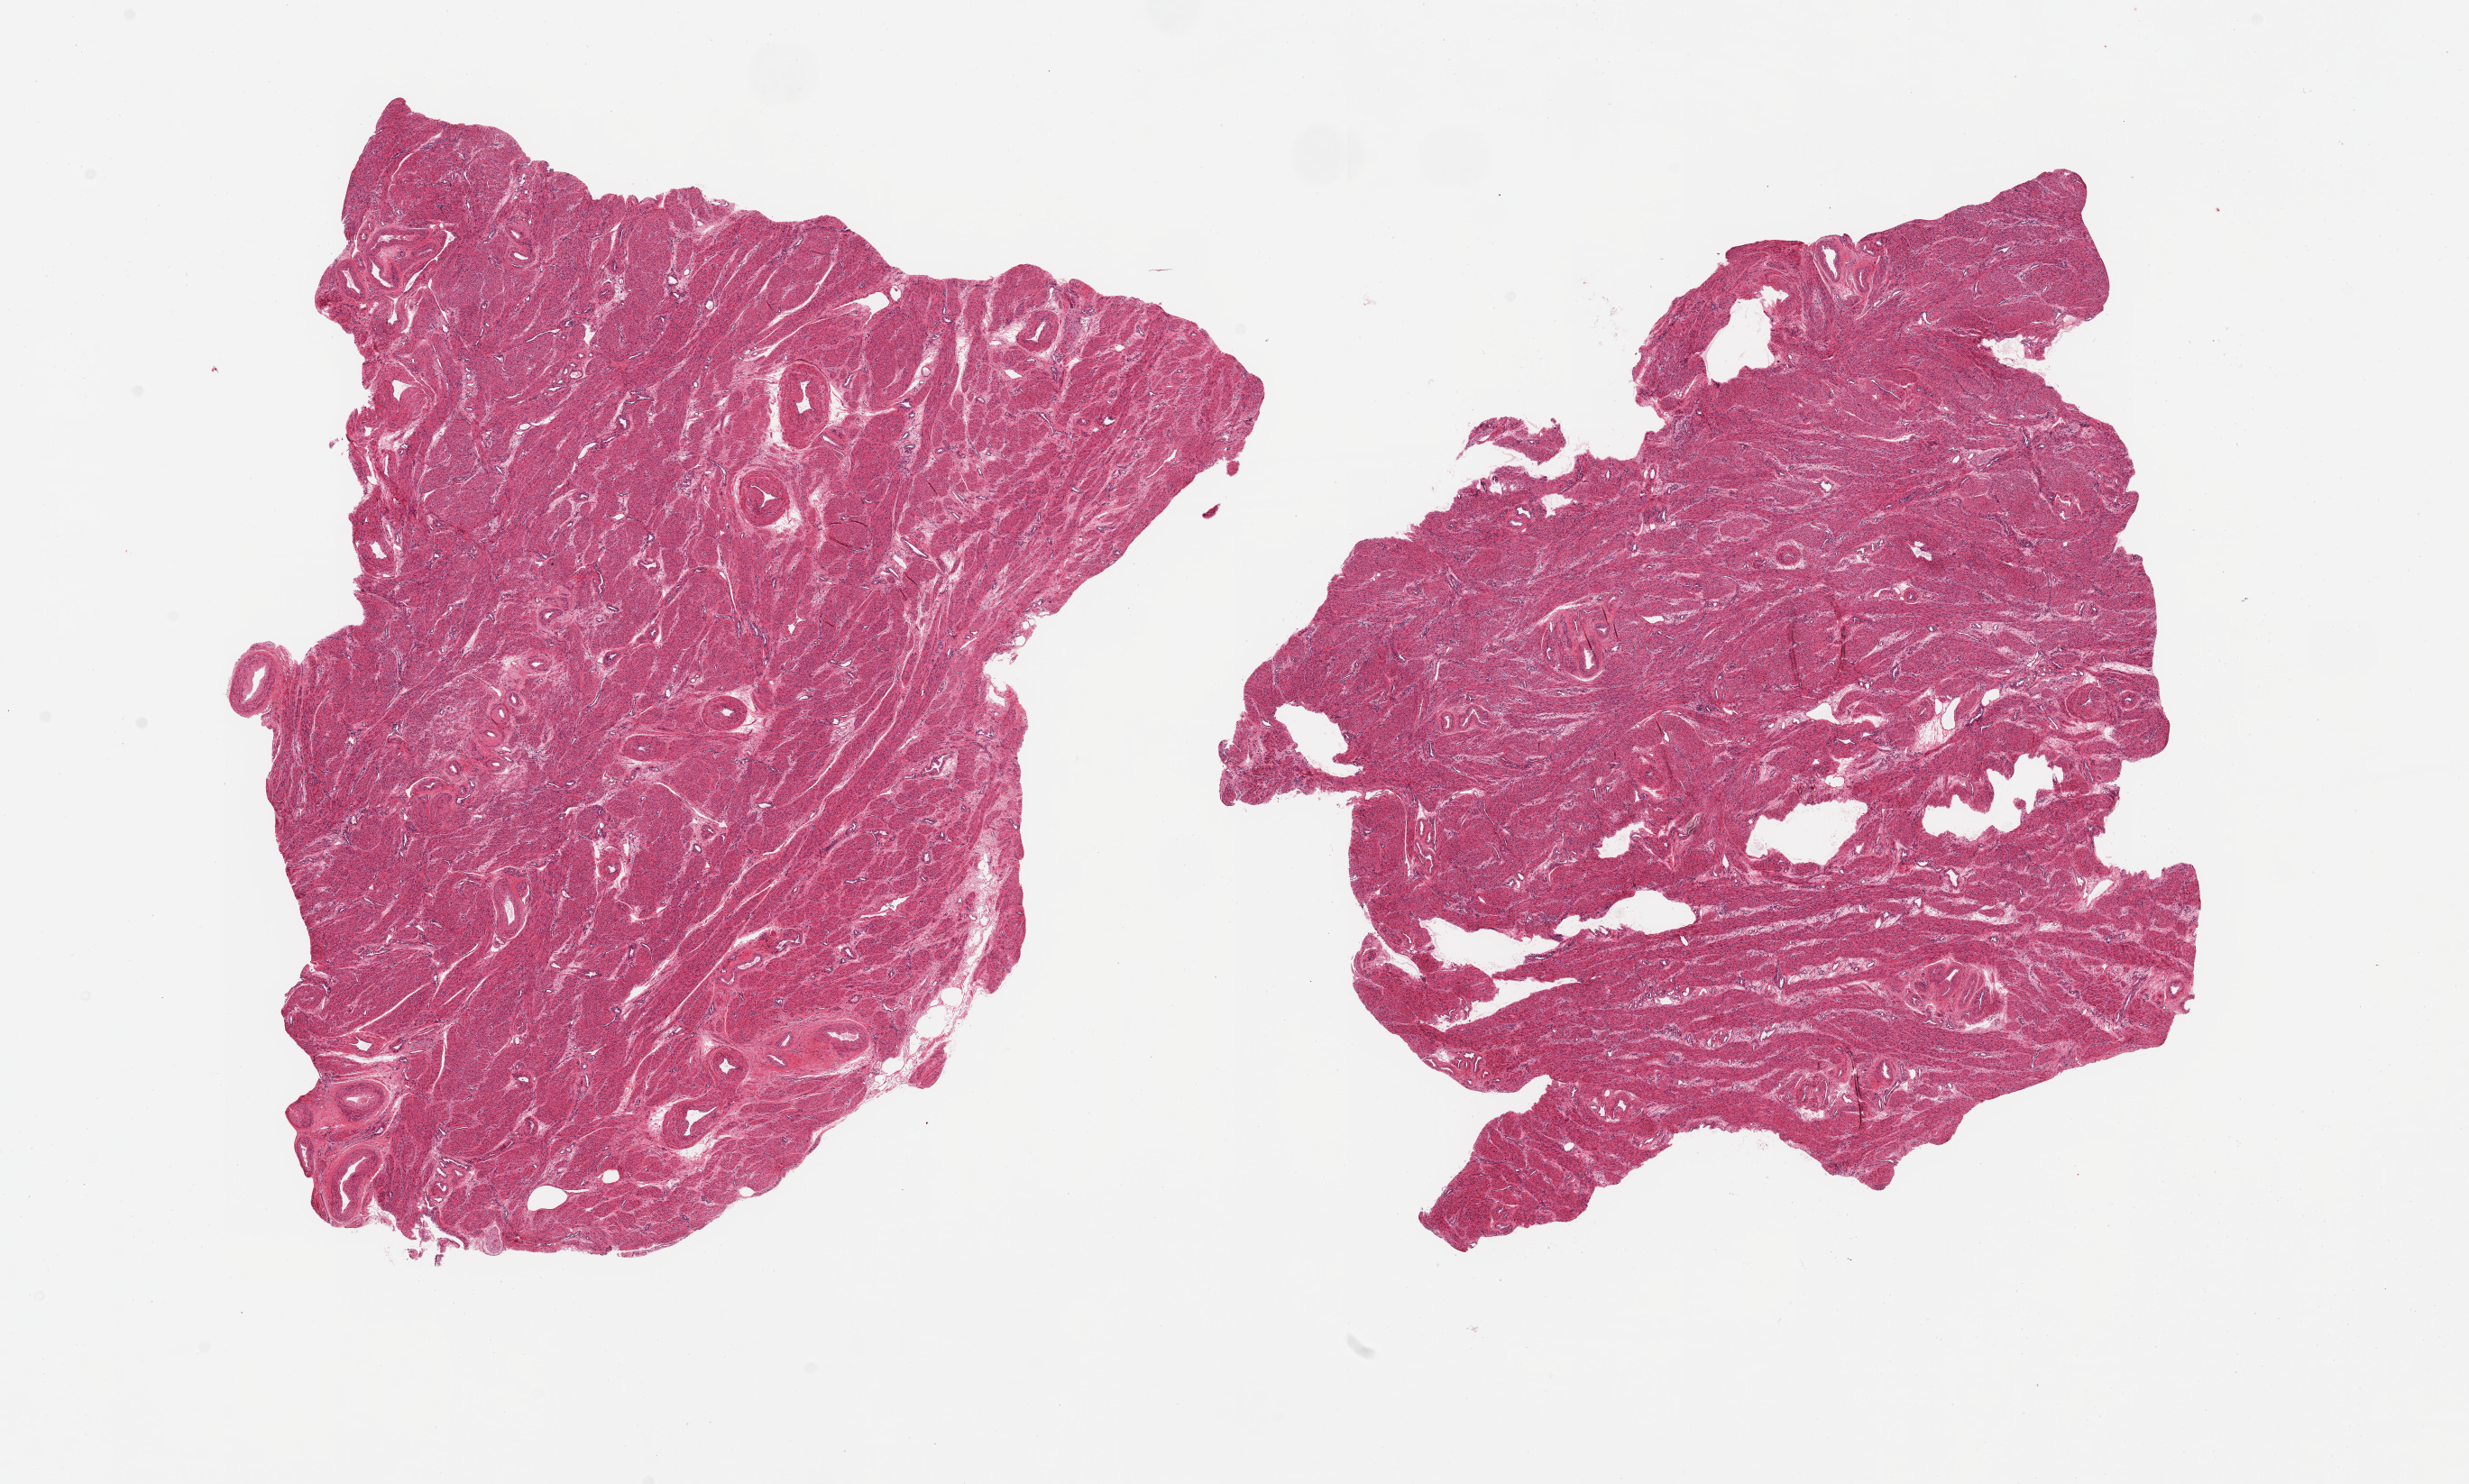
Digitized H&E-stained section, brightfield, shown as a low-resolution overview of the whole scanned area (about 21.7 x 13.0 mm, from a 20x scan). PAXgene-fixed paraffin-embedded (PFPE) section. Sampled site (target tissue): uterus. Tissue donor sample.
Review note (as recorded): 2 pieces; myometrium only in this section.